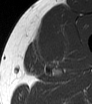
MRI of an extremity soft-tissue mass, one axial slice. Position 42 of 62 along the scan axis. MR volume resampled by the dataset authors to the PET/CT grid (not the native acquisition matrix). 92 × 104 image matrix, field of view 90 × 102 mm. Male patient. Case-level facts recorded for this patient, not image findings: histological type: mixoid liposarcoma; grade: low; site of the primary tumour: left thigh.
Structures marked on this image (expert contour drawn on MRI and transferred to this co-registered scan by the dataset authors):
- gross tumour volume (mass): bounding box <32,33,65,66> (left, top, right, bottom; pixels)